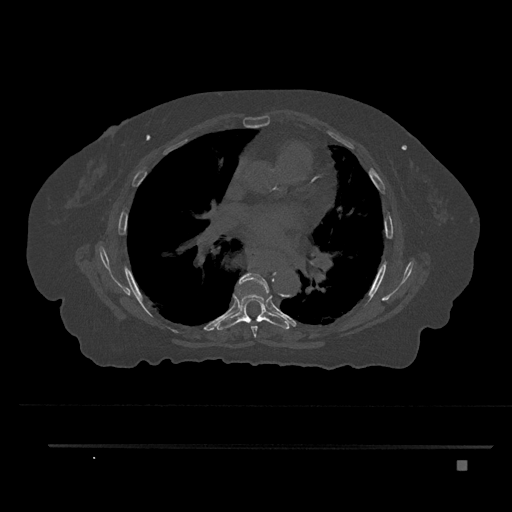
CT including the spine, one axial slice. Position 501 of 797 along the scan axis. 120 kVp. Bone window (W 1800 / L 400 HU). 512 × 512 image matrix, field of view 437 × 437 mm. Patient: female, 76 years. Case-level facts recorded for this patient, not image findings: primary cancer: lung; vertebrae with lytic lesions (as recorded): T11, L3.
Annotated regions visible in this slice (semi-automatically segmented with operator editing):
- T6 vertebra: bounding box [x1, y1, x2, y2] px = [238, 272, 269, 337]
- T7 vertebra: [216, 295, 290, 330]